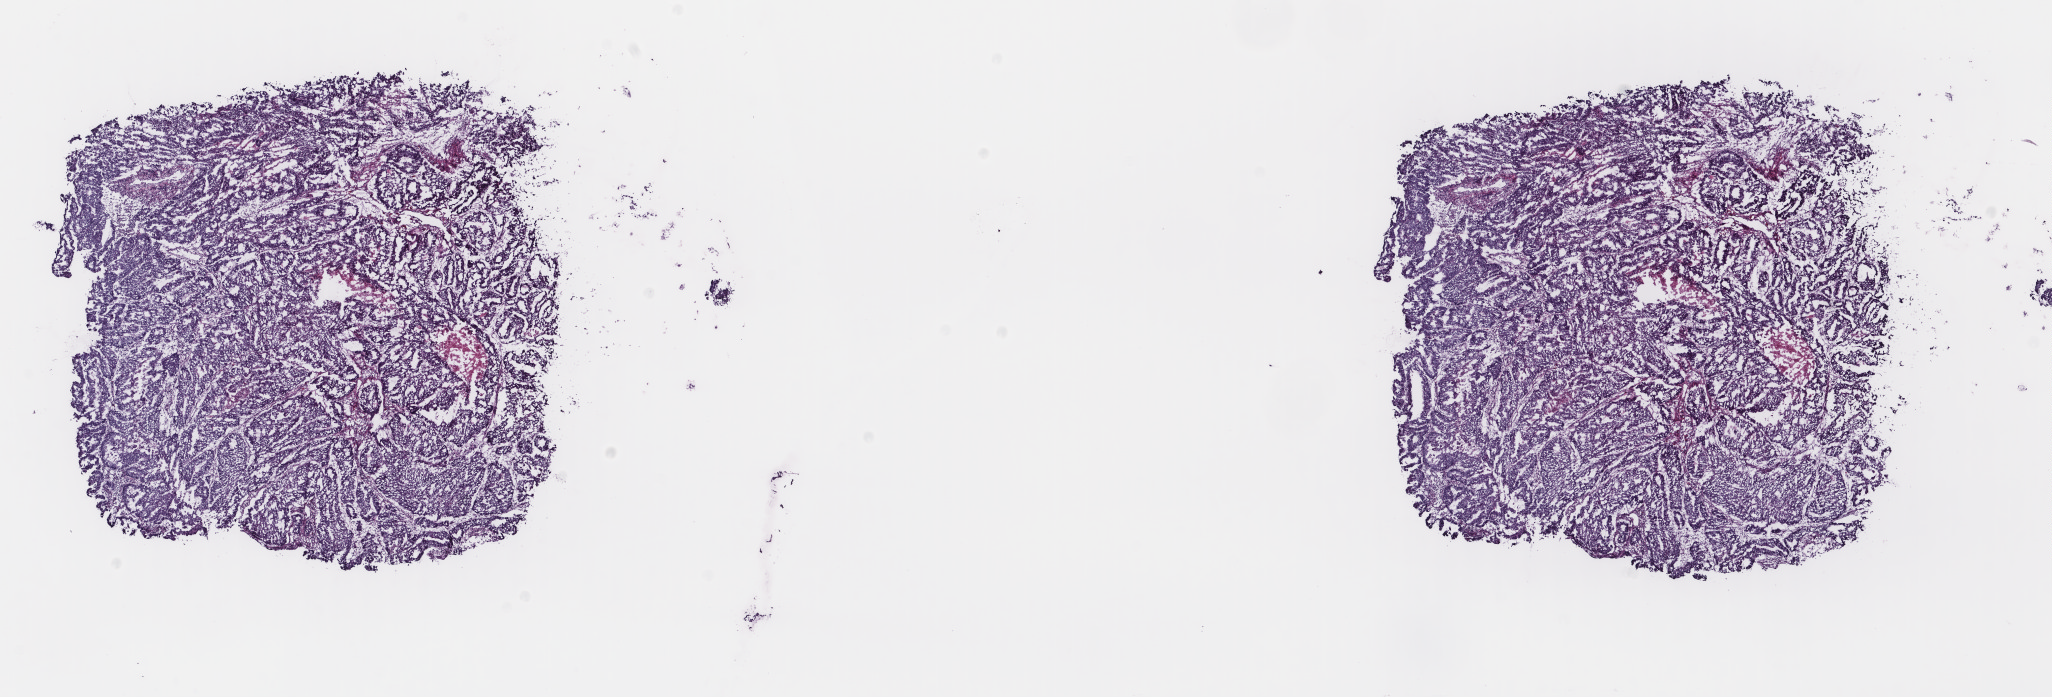
Digitized H&E-stained tissue section (whole slide) — a low-resolution overview of the entire scanned area, about 16.3 x 5.5 mm (slide scanned at 40x). Frozen section from the top of the tissue portion. Uterus, primary tumour sample. Female patient; age at initial diagnosis 57 years. Composition of this section per pathologist review: tumour cells 70%, tumour nuclei 70%.
Diagnosis: Endometrioid adenocarcinoma, NOS.